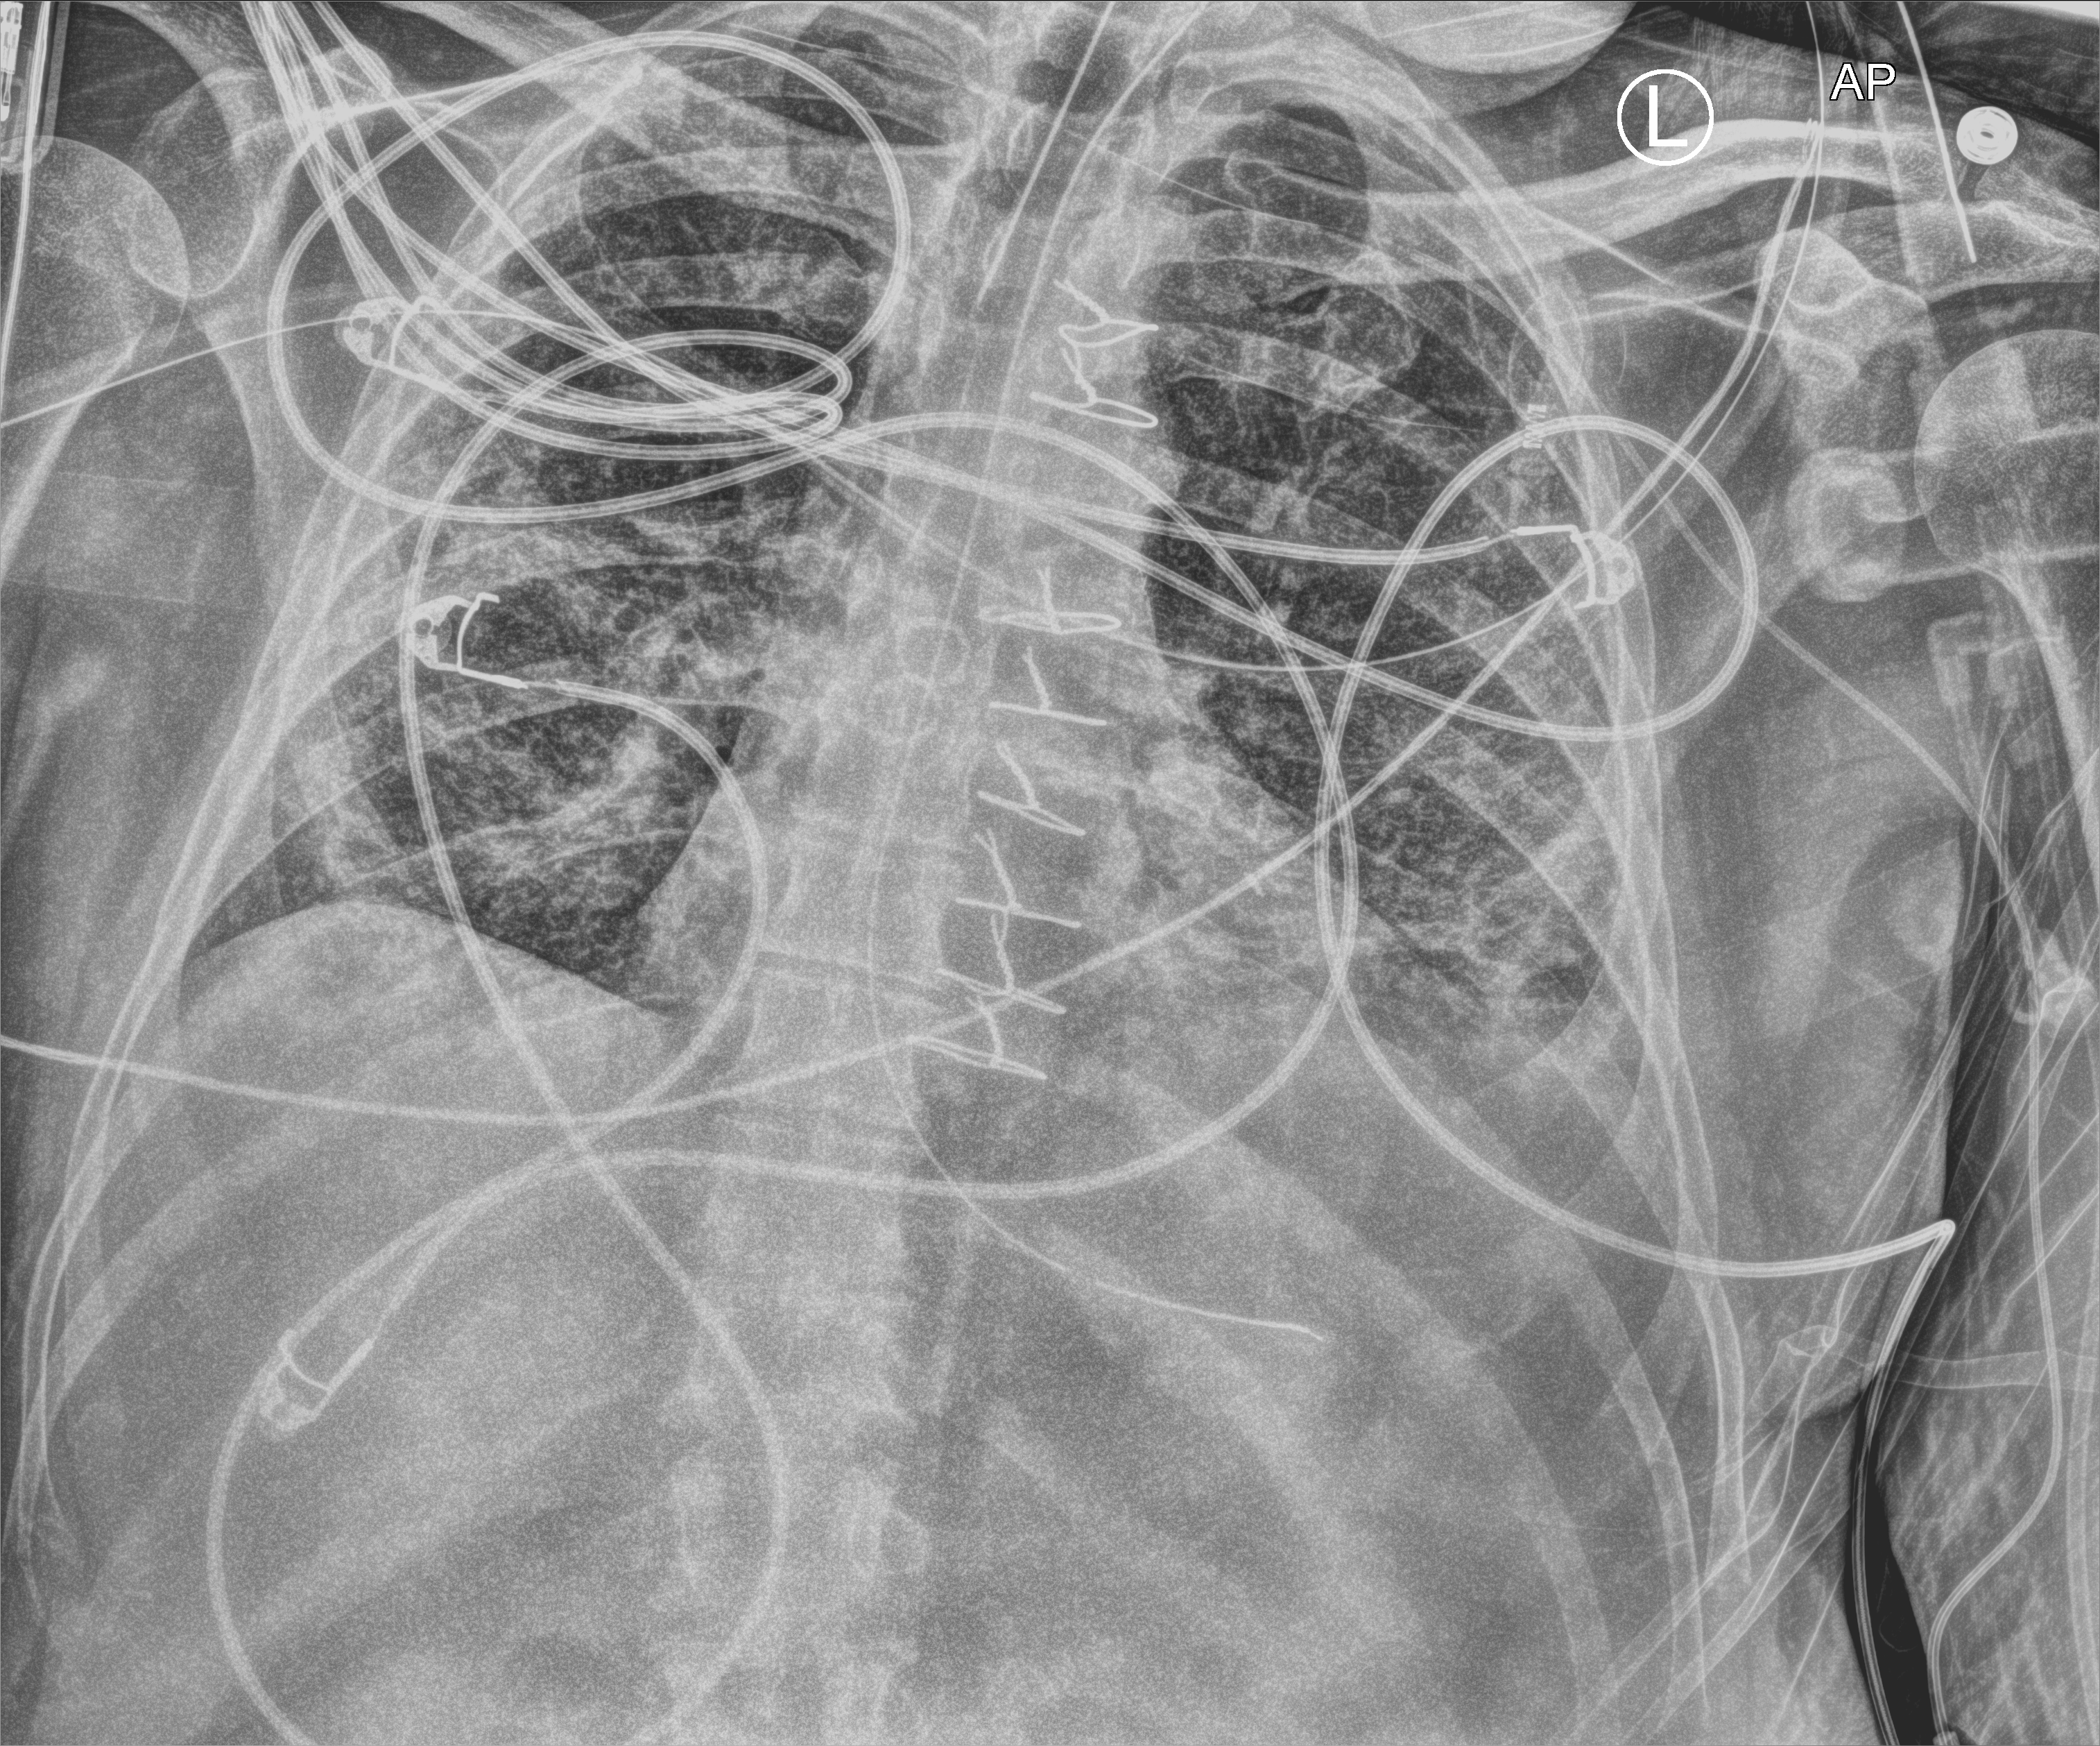
Chest X-ray (portable), anteroposterior (AP) projection. Patient hospitalised with COVID-19; male, aged 18–59 years.
Admission-level facts for this patient (not findings on this image; timing relative to this image not recorded):
- admitted to intensive care during this hospital stay: yes